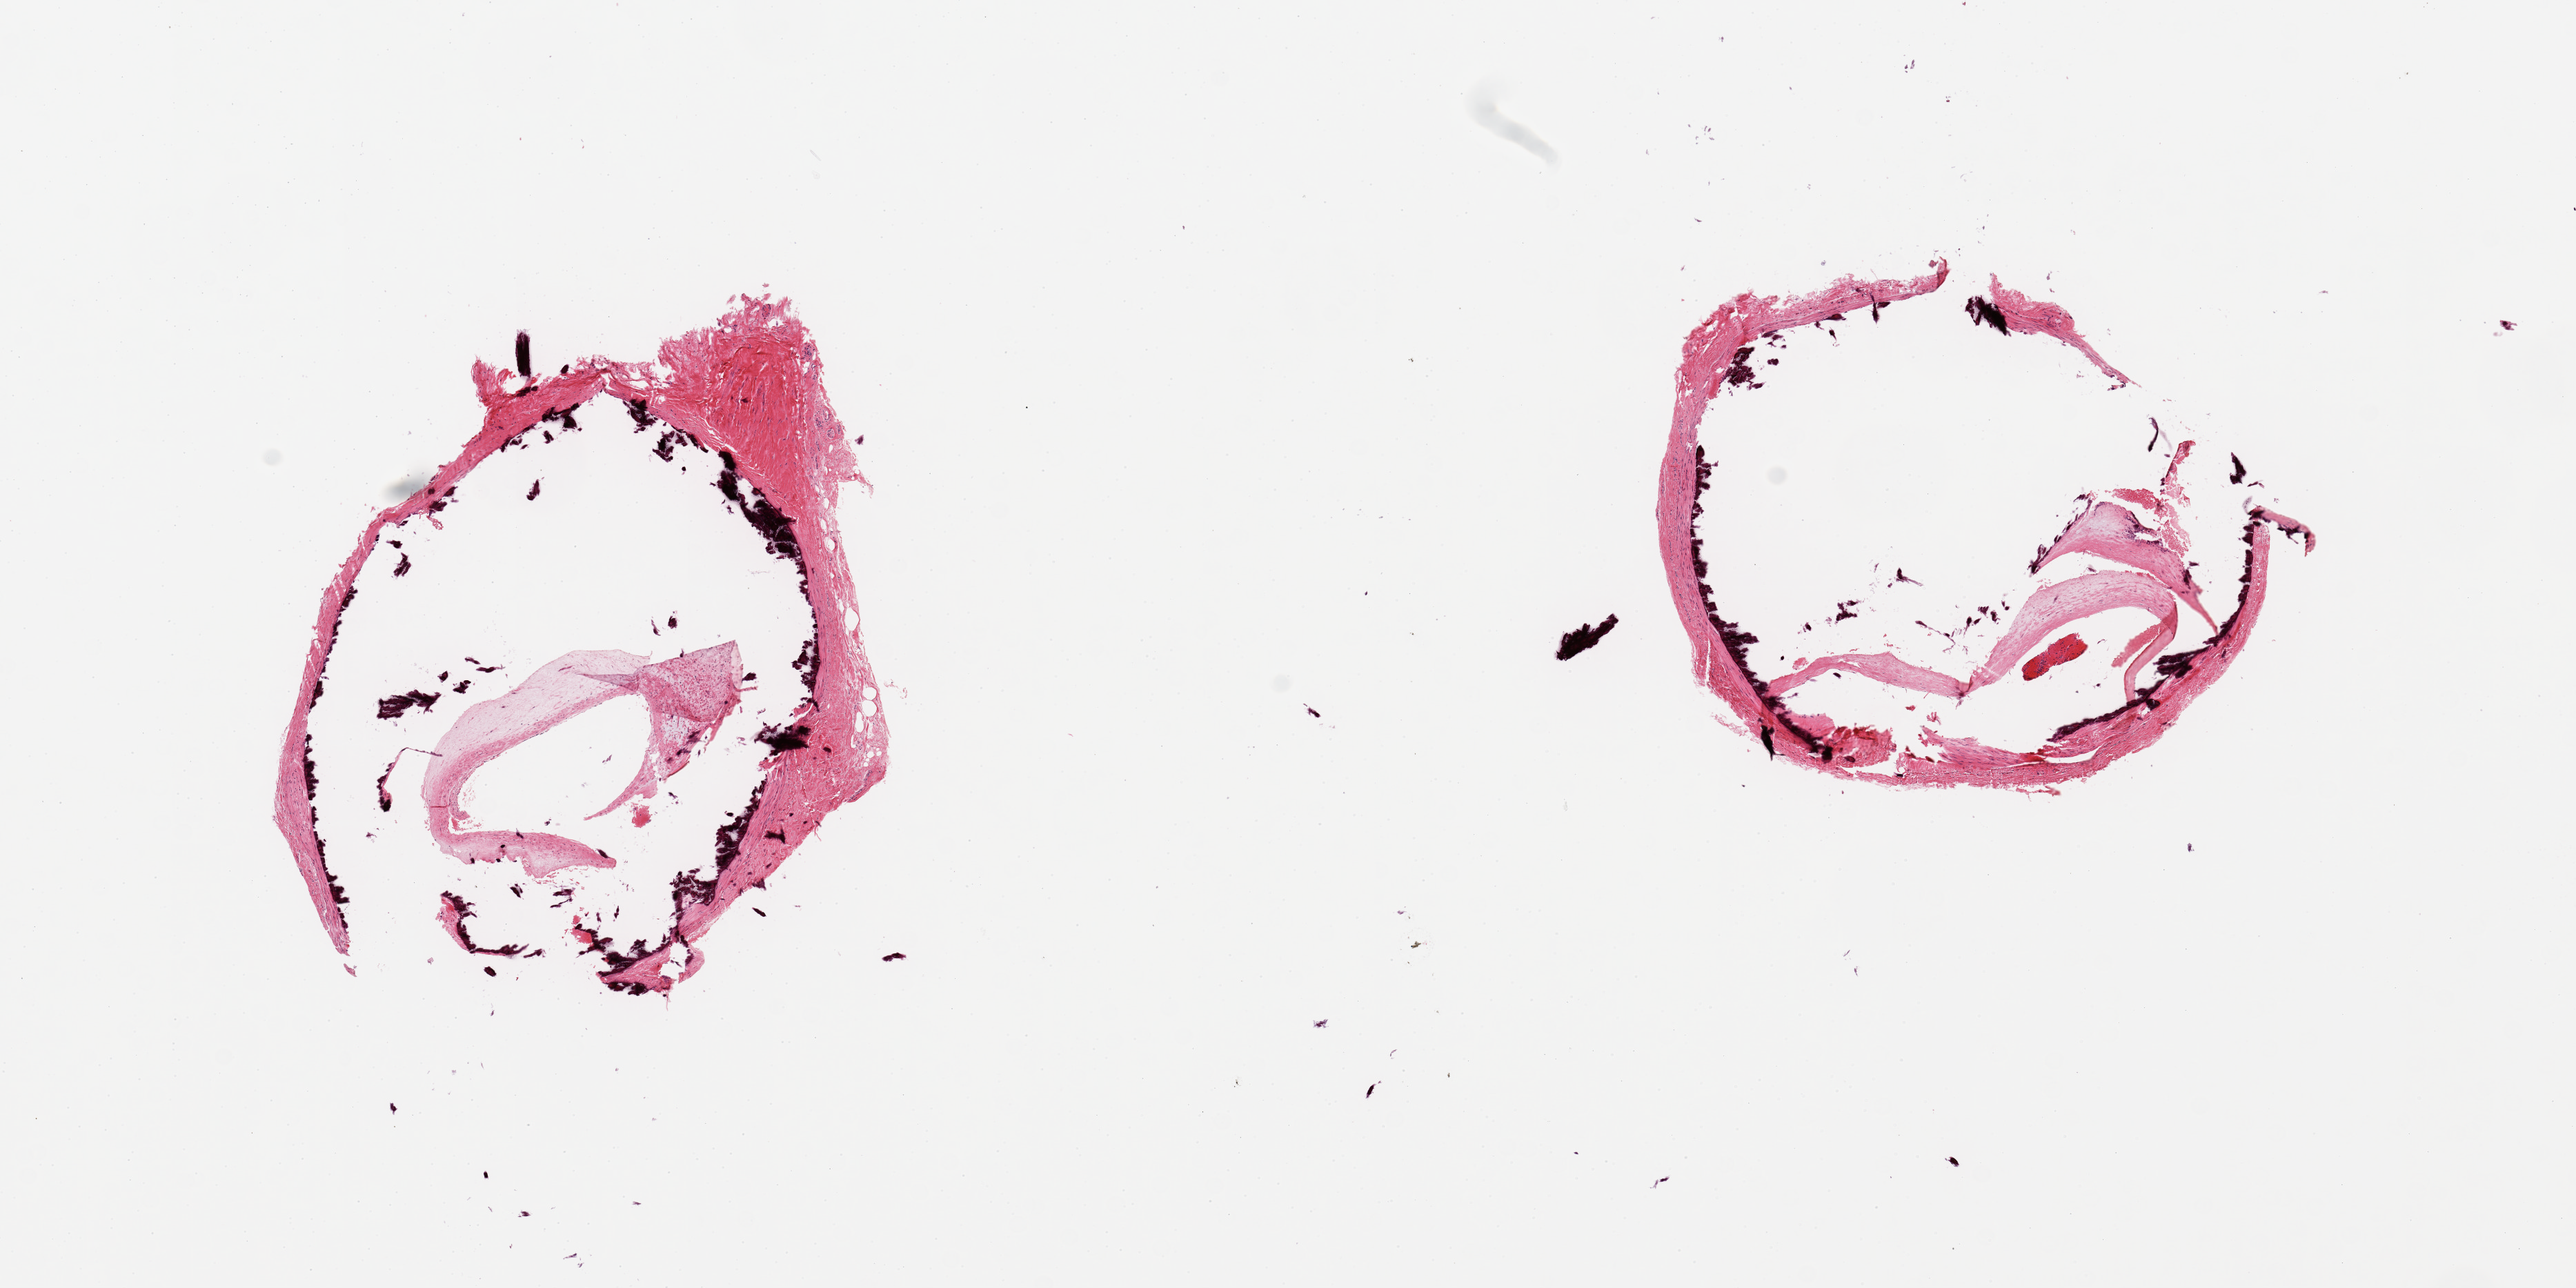
H&E whole-slide image, low-resolution overview of the scanned area, about 14.8 x 7.4 mm. PAXgene-fixed, paraffin-embedded tissue. Sampled site (target tissue): tibial artery. Tissue donor sample. Donor sex: male.
Pathologist's review note for this sample: 2 pieces extensive mural calcifications, atherosis vs Monckeberg type.